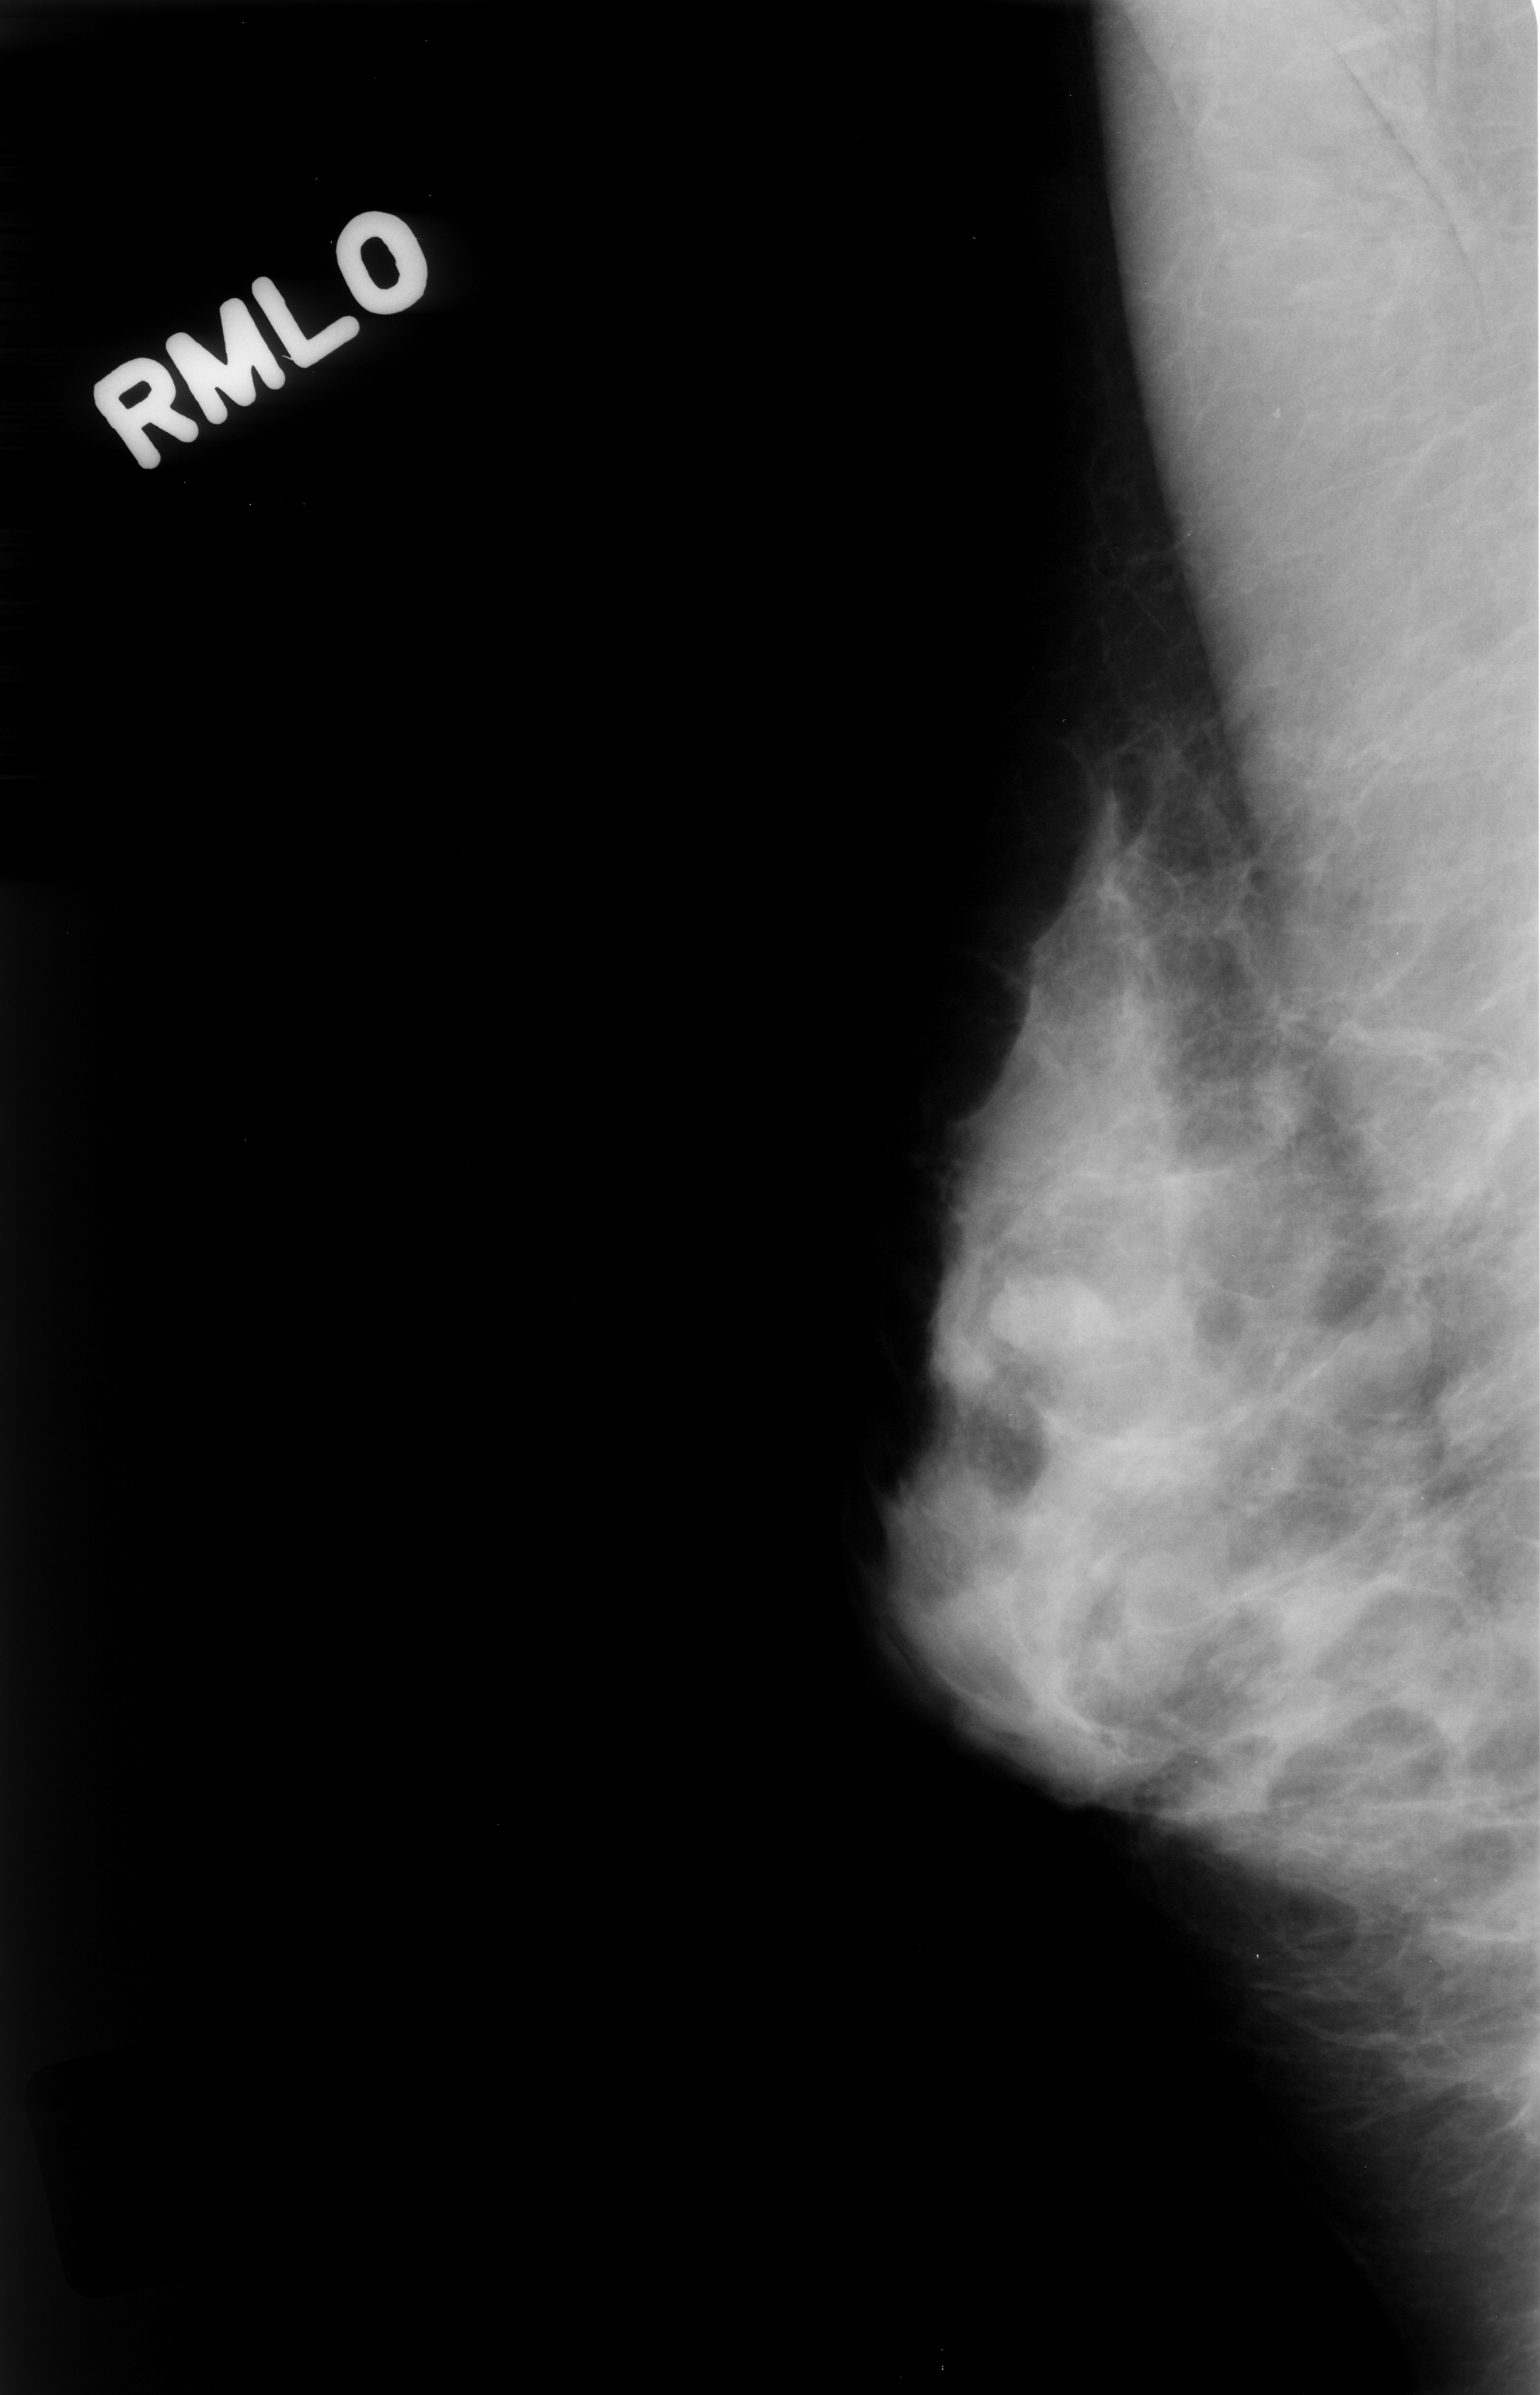
Scanned film-screen mammogram; right breast; mediolateral oblique (MLO) view; breast composition: heterogeneously dense (BI-RADS density category 3 of 4).
Radiologist-marked abnormalities on this image: mass, shape oval, margins circumscribed; BI-RADS assessment category 4; subtlety rating 5 on a 1 (subtle) to 5 (obvious) scale; pathology result (as recorded, not read from the image): benign.